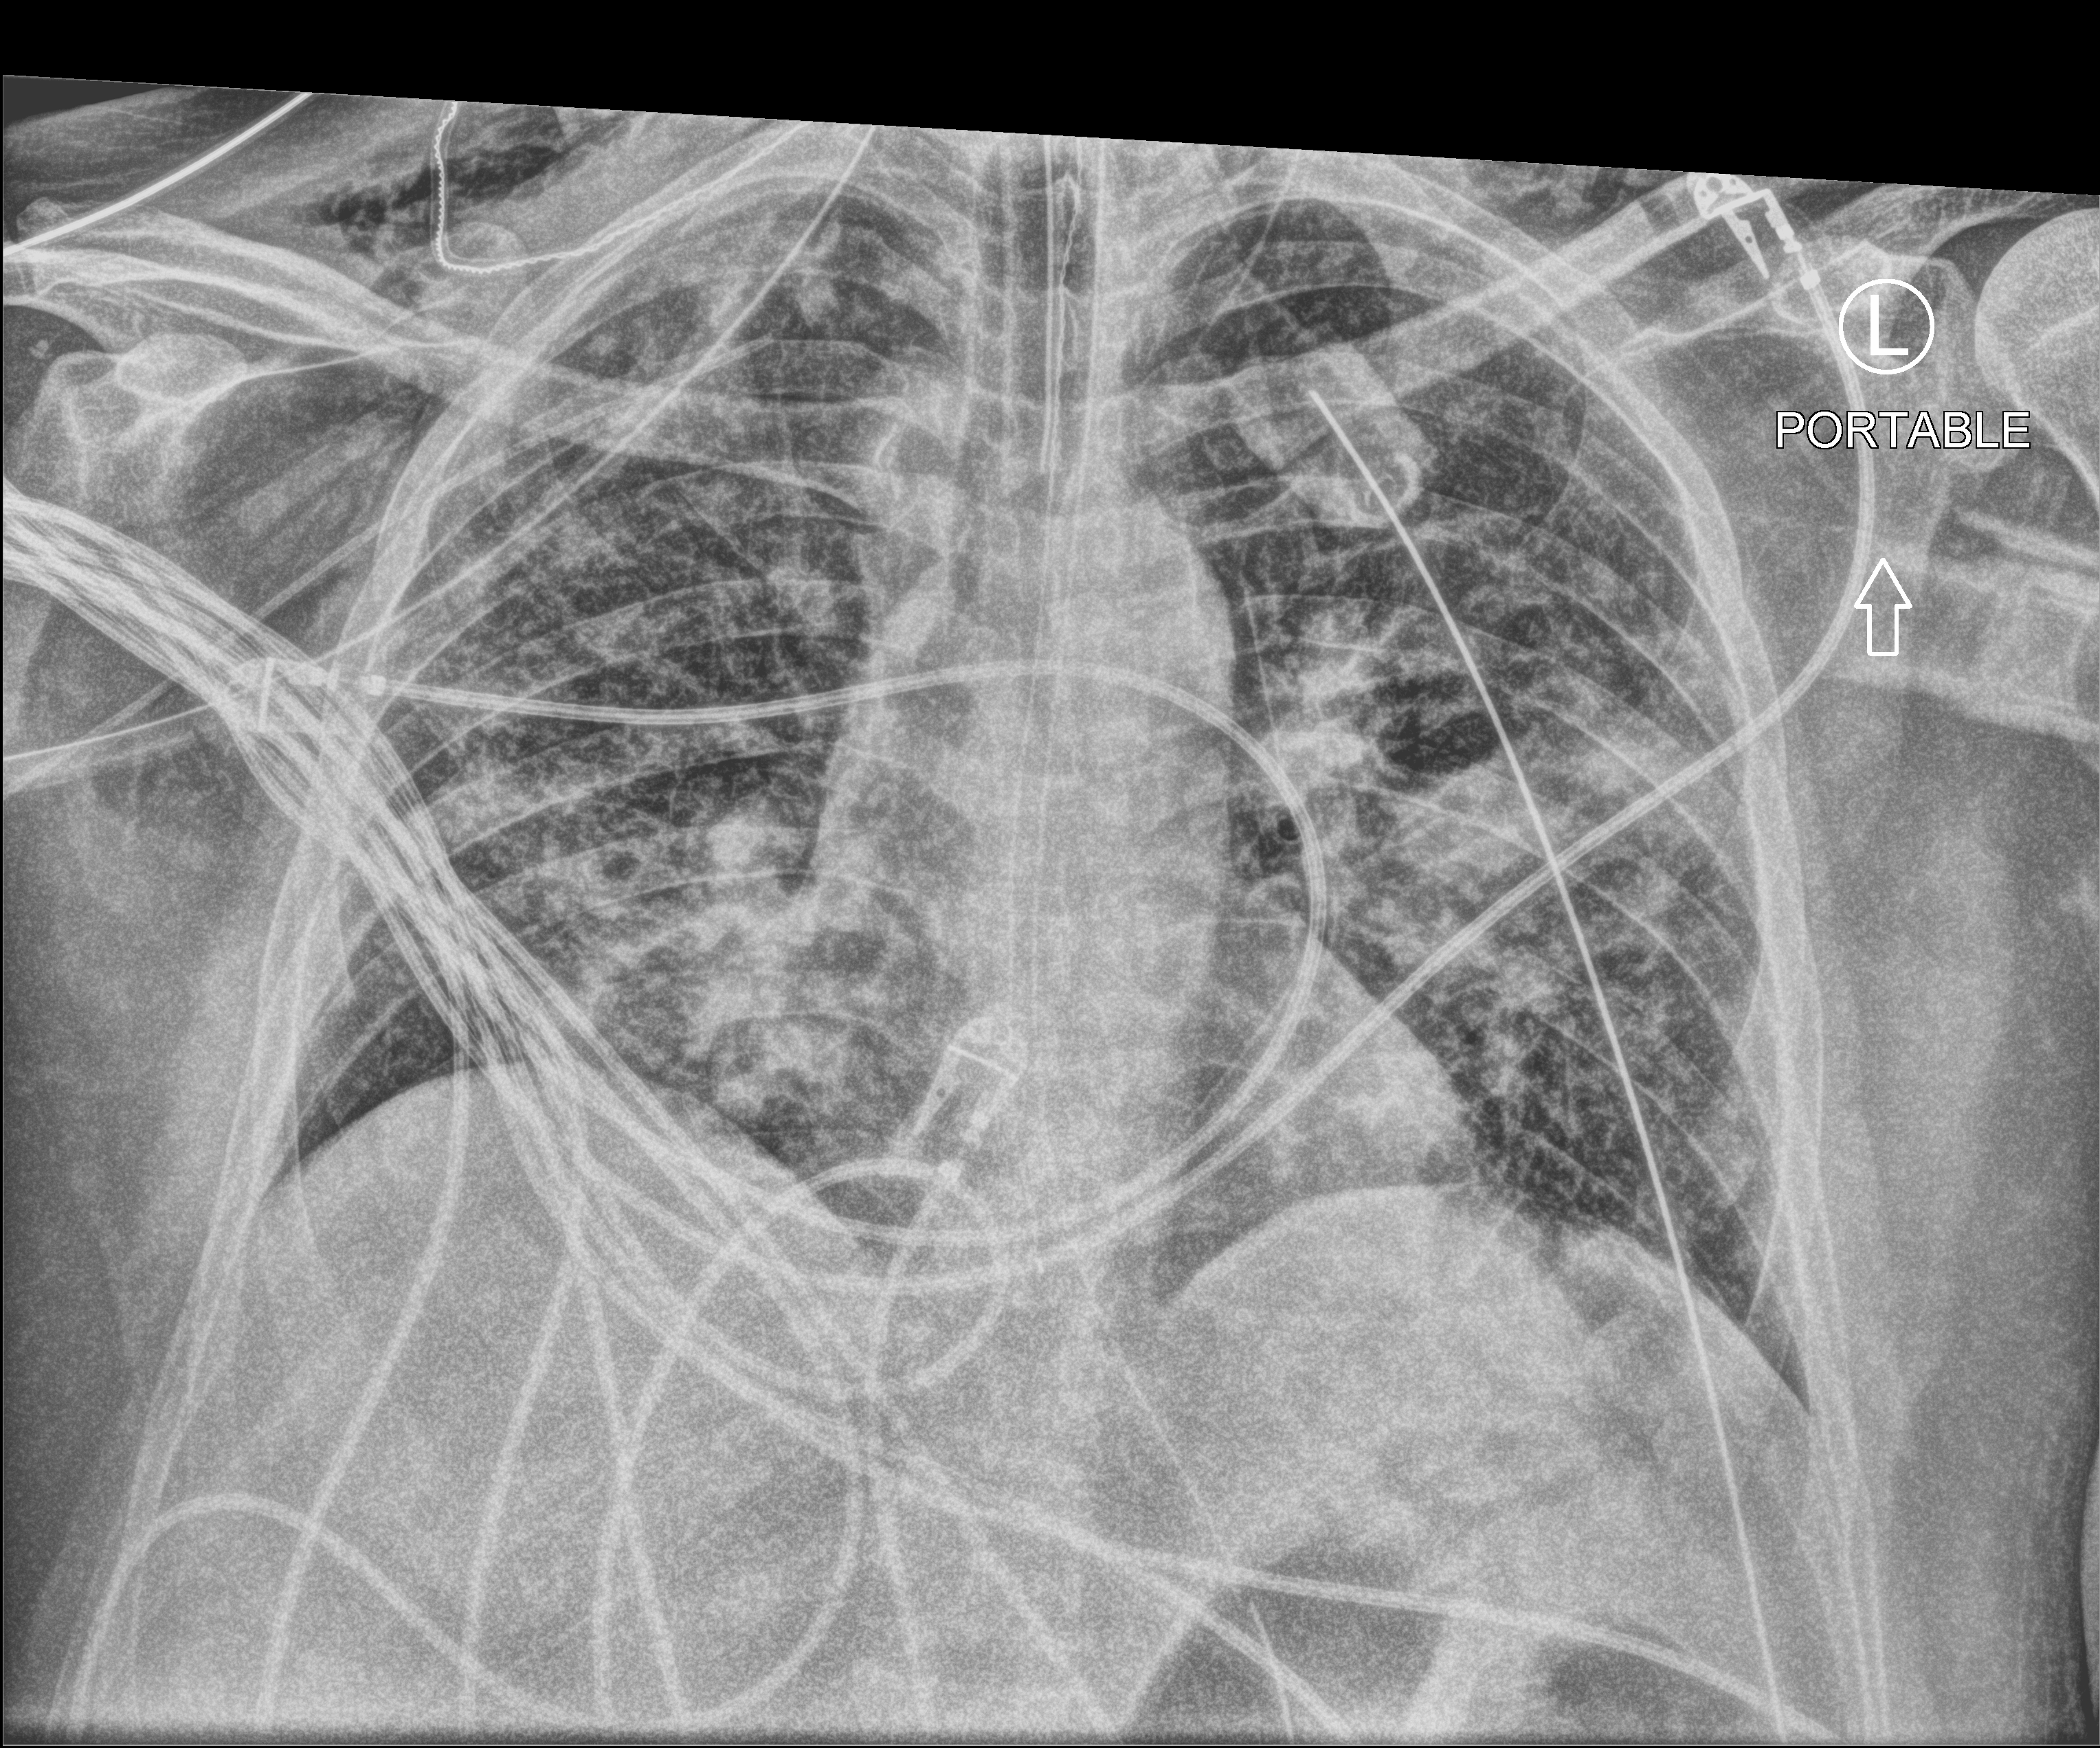
Portable chest radiograph, anteroposterior (AP) projection. Adult patient hospitalised with COVID-19, age 18–59 years.
Admission-level facts for this patient (not findings on this image; timing relative to this image not recorded): COPD (admission record): no; admitted to intensive care during this hospital stay: yes.